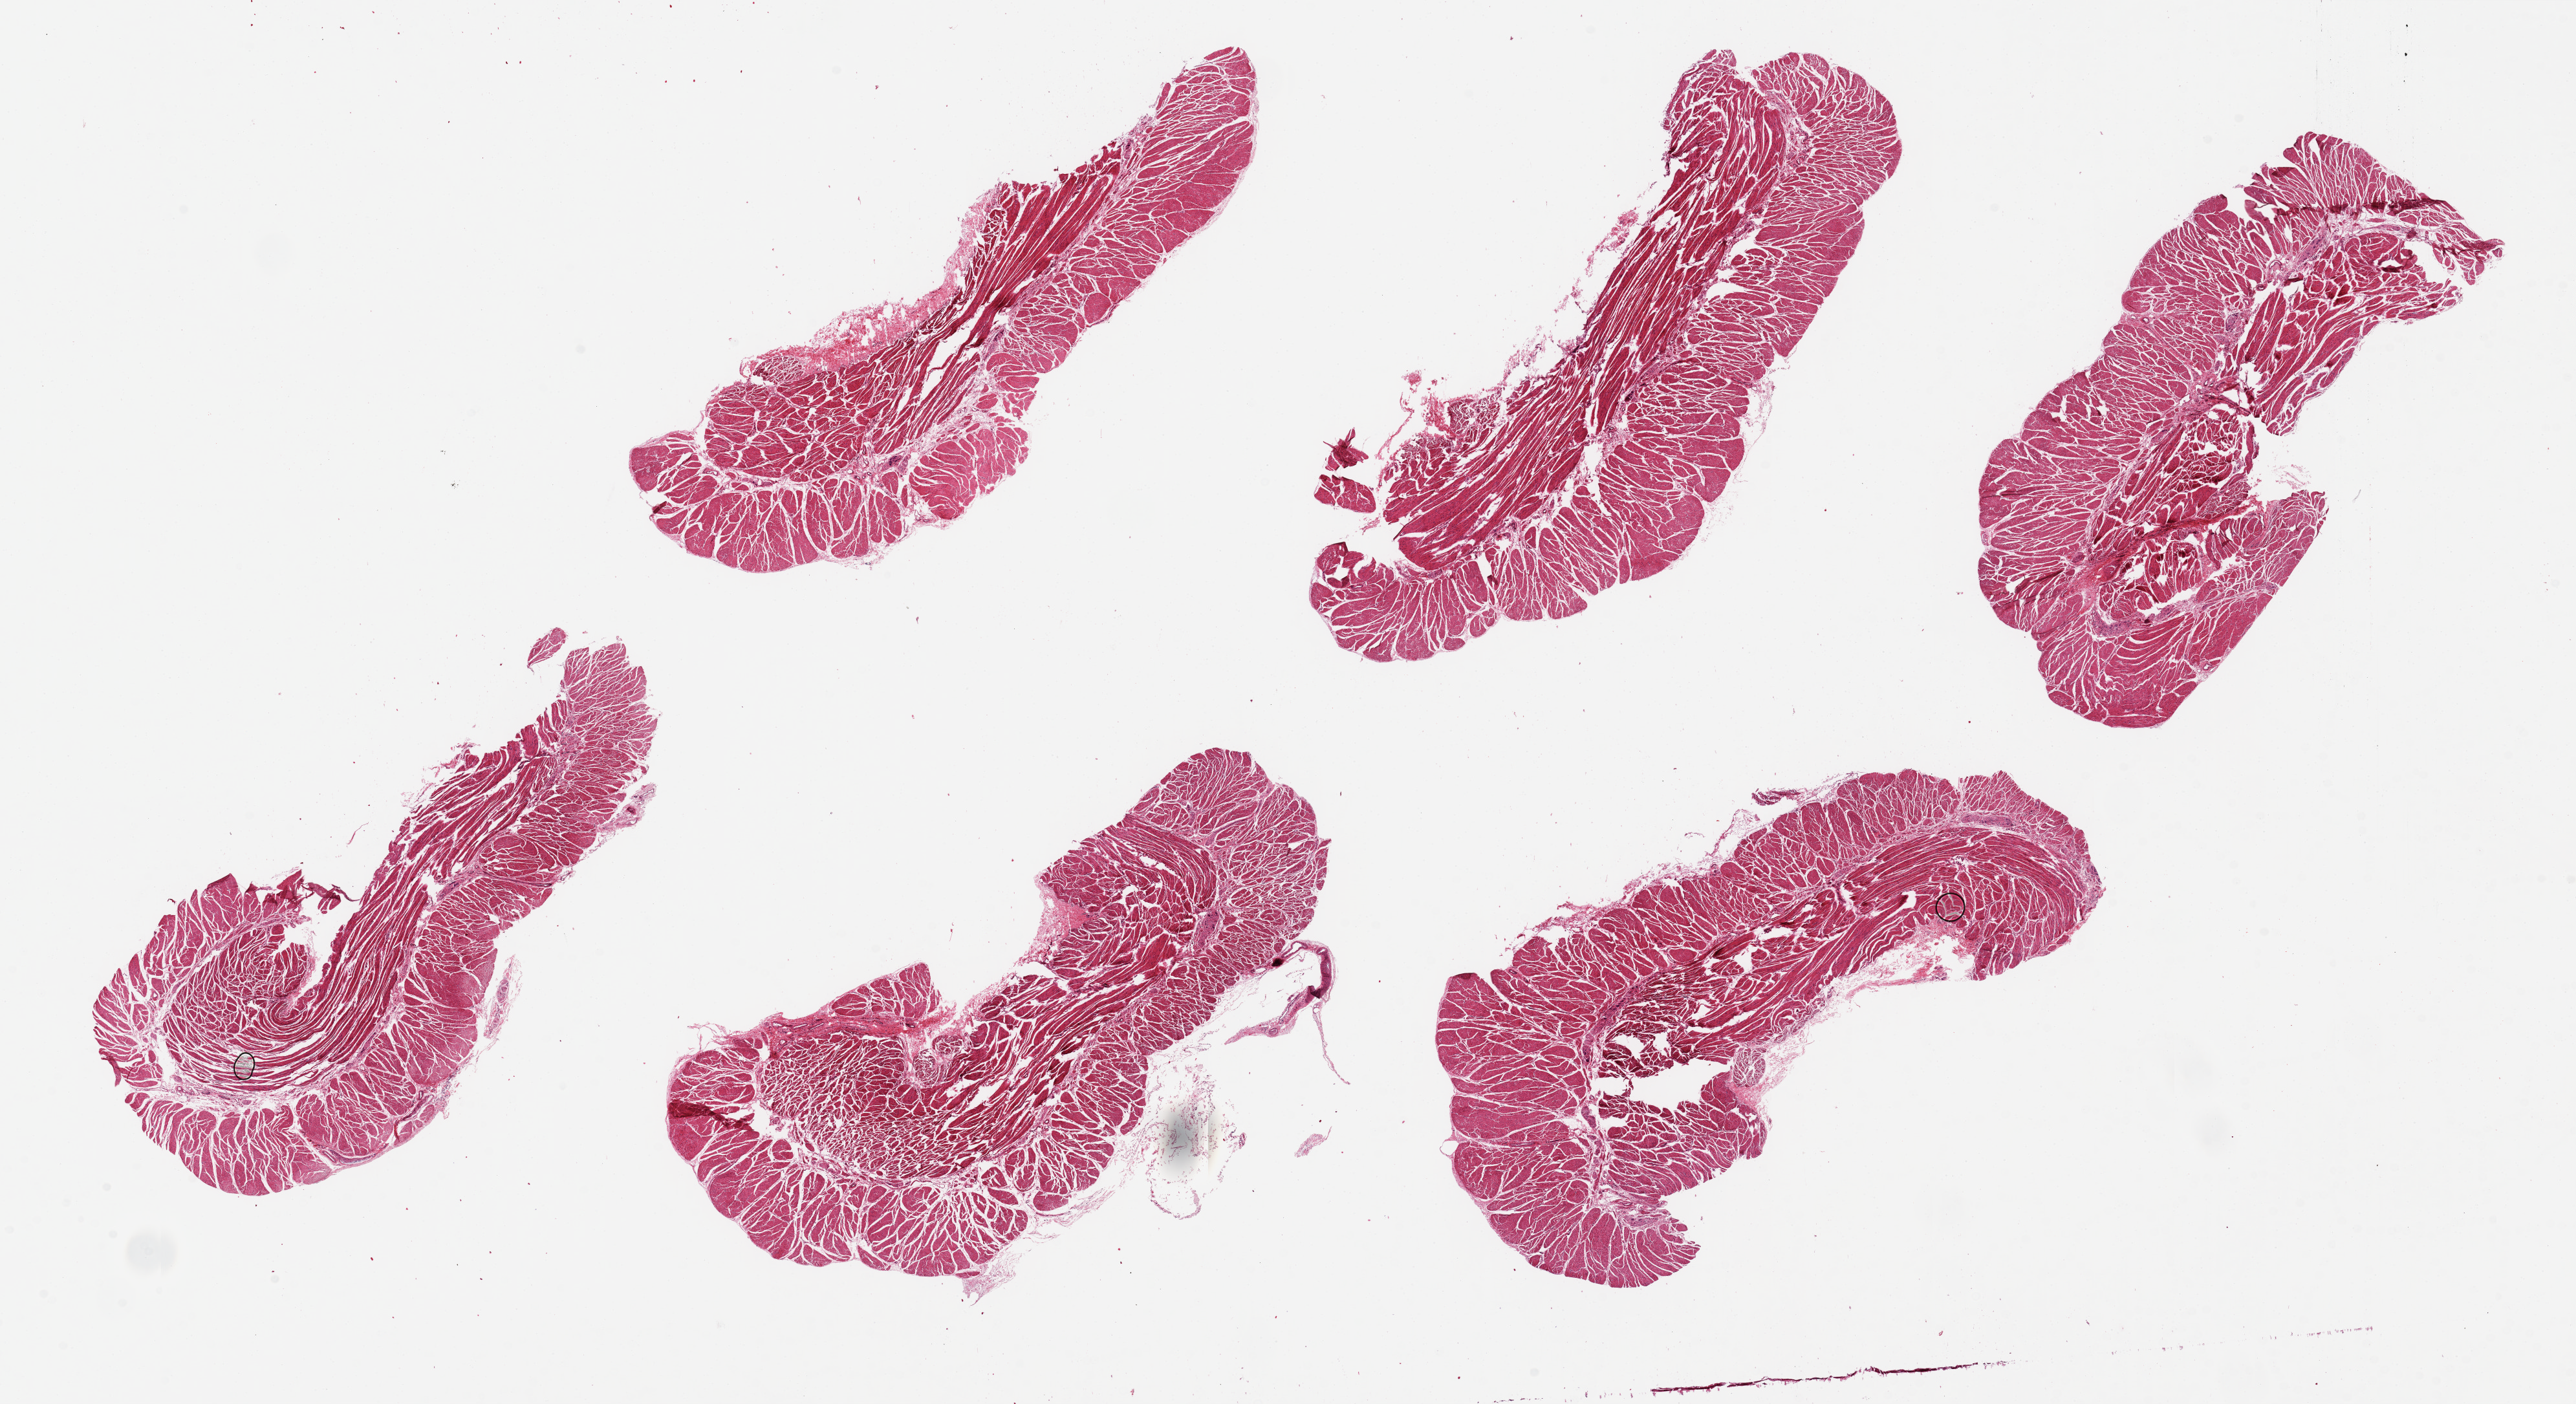
Digitized hematoxylin and eosin (H&E)-stained section, brightfield, low-resolution overview of the scanned area, about 31.5 x 17.2 mm (slide scanned at 20x), PAXgene-fixed, paraffin-embedded tissue, target tissue: esophageal muscle, donor tissue sample. Donor sex: female.
Pathologist's review note for this sample: 6 pieces, up to 9x4mm; all muscle good specimens.